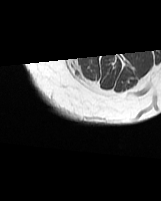
MRI of an extremity soft-tissue mass, one axial slice. Position 5 of 70 along the scan axis. MR volume resampled by the dataset authors to the PET/CT grid (not the native acquisition matrix). 3.27 mm slice thickness. 161 × 201 image matrix. Female patient. Case-level facts recorded for this patient, not image findings: histological type: synovial sarcoma; grade: intermediate; site of the primary tumour: right buttock.
Outlined on this slice (expert contour drawn on MRI and transferred to this co-registered scan by the dataset authors):
- gross tumour volume including surrounding oedema: bounding box (x1, y1, x2, y2) in pixels: (67, 59, 82, 80)